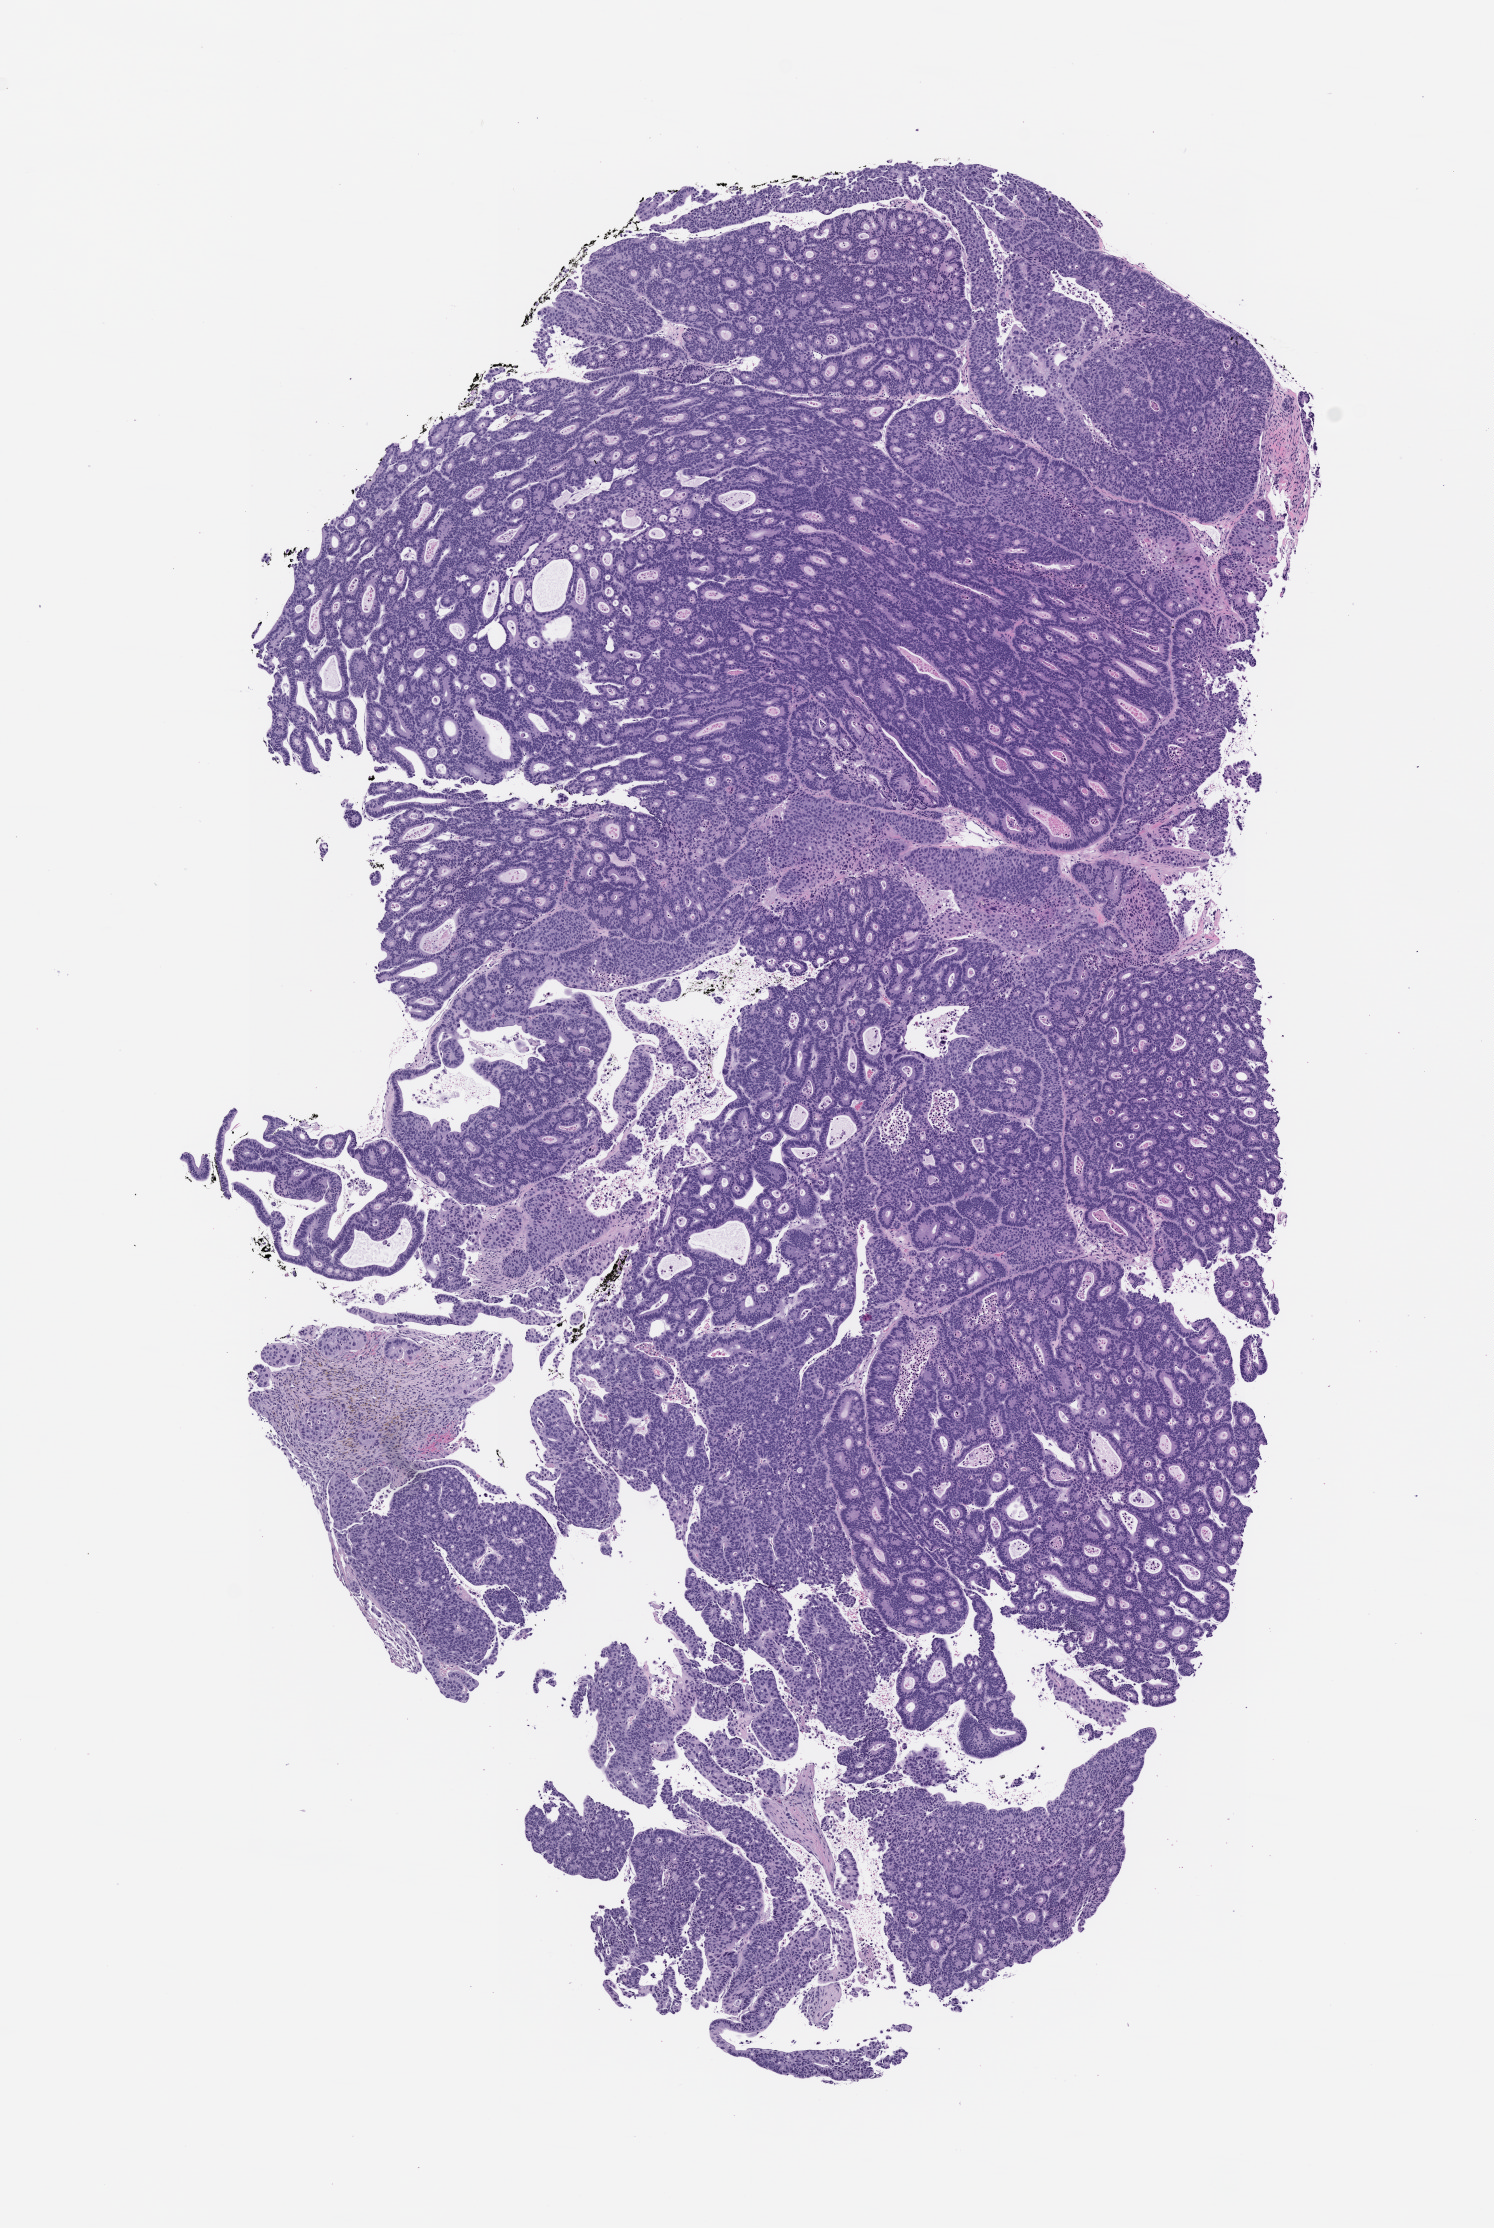
Hematoxylin and eosin (H&E) whole-slide image of a patient-derived xenograft (PDX) tumor grown in a mouse, passage 3, low-resolution overview of the scanned area, about 6.0 x 9.0 mm; FFPE section; tumor site category: colon.
• originating patient diagnosis: Colon Adenocarcinoma